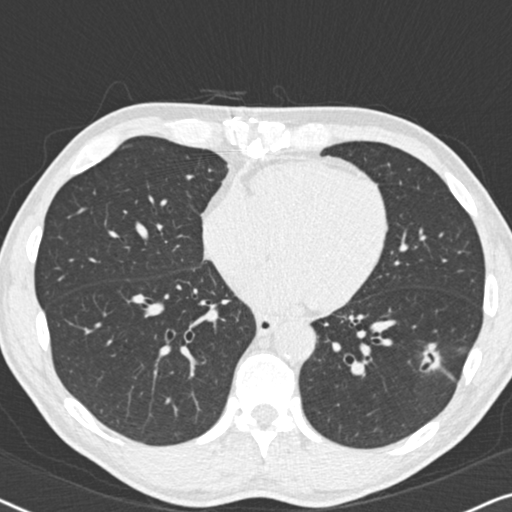
Axial slice from a low-dose chest CT screening exam. Second screening round (one year after baseline). Lung window (W 1500 / L -600 HU). Standard (soft-tissue) reconstruction kernel (B30f). Slice 120 of 208 in the series. 512 × 512 image matrix. Male participant, aged 59 years at enrolment. Current smoker at enrolment.
Expert reader's lesion annotation, bounding box [x1, y1, x2, y2] px = [412, 336, 463, 382]. The screening reader recorded 2 non-calcified nodules or masses ≥4 mm on this exam (left lower lobe, right middle lobe); which of them this box marks is not recorded.